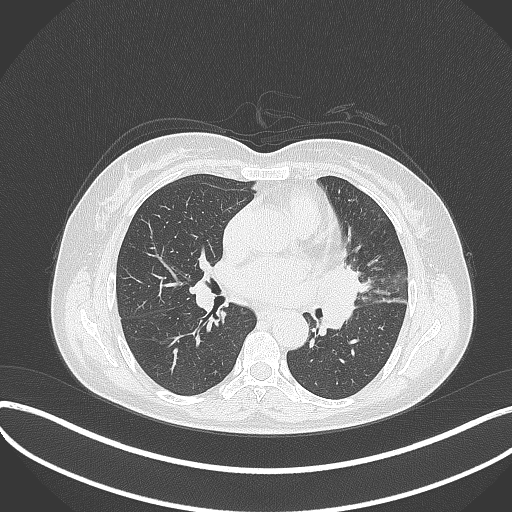
Chest CT, one axial slice; slice 182 of 373 in the series (ordered by position); 120 kVp; lung window (W 1500 / L -600 HU); 1 mm slice thickness; 512 × 512 image matrix. Patient: female, 54 years. From the clinical record (not read from this slice): clinical TNM (as recorded): T2a N1 M0; histopathological grade: G3.
Annotated regions visible in this slice (bounding box drawn by a radiologist):
- lung tumour (recorded histology: small cell carcinoma): bounding box (x1, y1, x2, y2) in pixels: (319, 259, 370, 337)